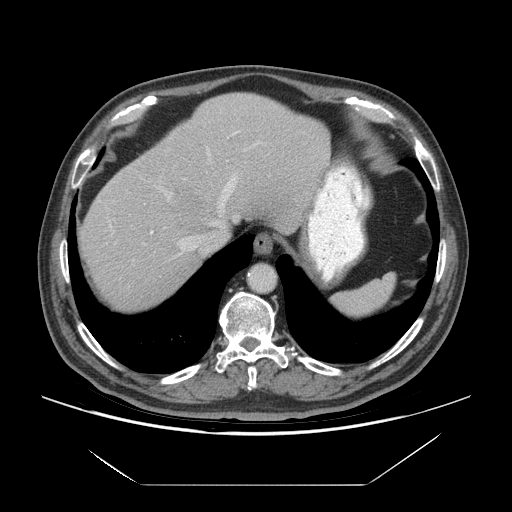
Contrast-enhanced abdominal CT (liver protocol), one axial slice; position 57 of 75 along the scan axis; reconstruction kernel STANDARD; 140 kVp; soft-tissue window (W 400 / L 40 HU); 512 × 512 image matrix, field of view 420 × 420 mm. Case-level facts recorded for this patient, not image findings: diagnosis: hepatocellular carcinoma (patient treated with transarterial chemoembolisation; whether this scan precedes or follows treatment is not stated here); TNM stage (as recorded): Stage-I; Child-Pugh class: A; tumour differentiation: well differentiated; tumour nodularity: uninodular.
Annotated regions visible in this slice (semi-automatically segmented with operator editing):
- abdominal aorta: bounding box <249,266,275,291> (left, top, right, bottom; pixels)
- liver parenchyma outside the tumour (the mass and vessels are separate outlines, so this box may not span the whole liver): <80,94,330,309>
- mass: <173,185,204,223>
- liver vessels: <110,131,261,255>